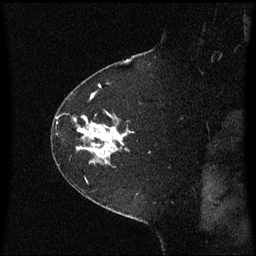
Breast MRI (dynamic contrast-enhanced), one sagittal slice. Position 49 of 60 along the scan axis. Dynamic contrast-enhanced series, image 2 of 3 at this slice position (ordered by acquisition). 1.5 T. TE 4.2 ms, TR 8.4 ms. 256 × 256 image matrix, field of view 210 × 210 mm. Female patient, age 60 years. Case-level facts recorded for this patient, not image findings: setting: breast cancer imaged before/during neoadjuvant chemotherapy; receptor status: triple-negative.
Outlined on this slice (semi-automatically segmented with operator editing):
- analysis volume of interest (the breast-tissue region the enhancement analysis was run in; not a lesion): bounding box (x1, y1, x2, y2) in pixels: (53, 108, 137, 182)
- tumour enhancement mask (voxels above the 70 % enhancement threshold inside the analysis volume of interest): (79, 124, 127, 158)